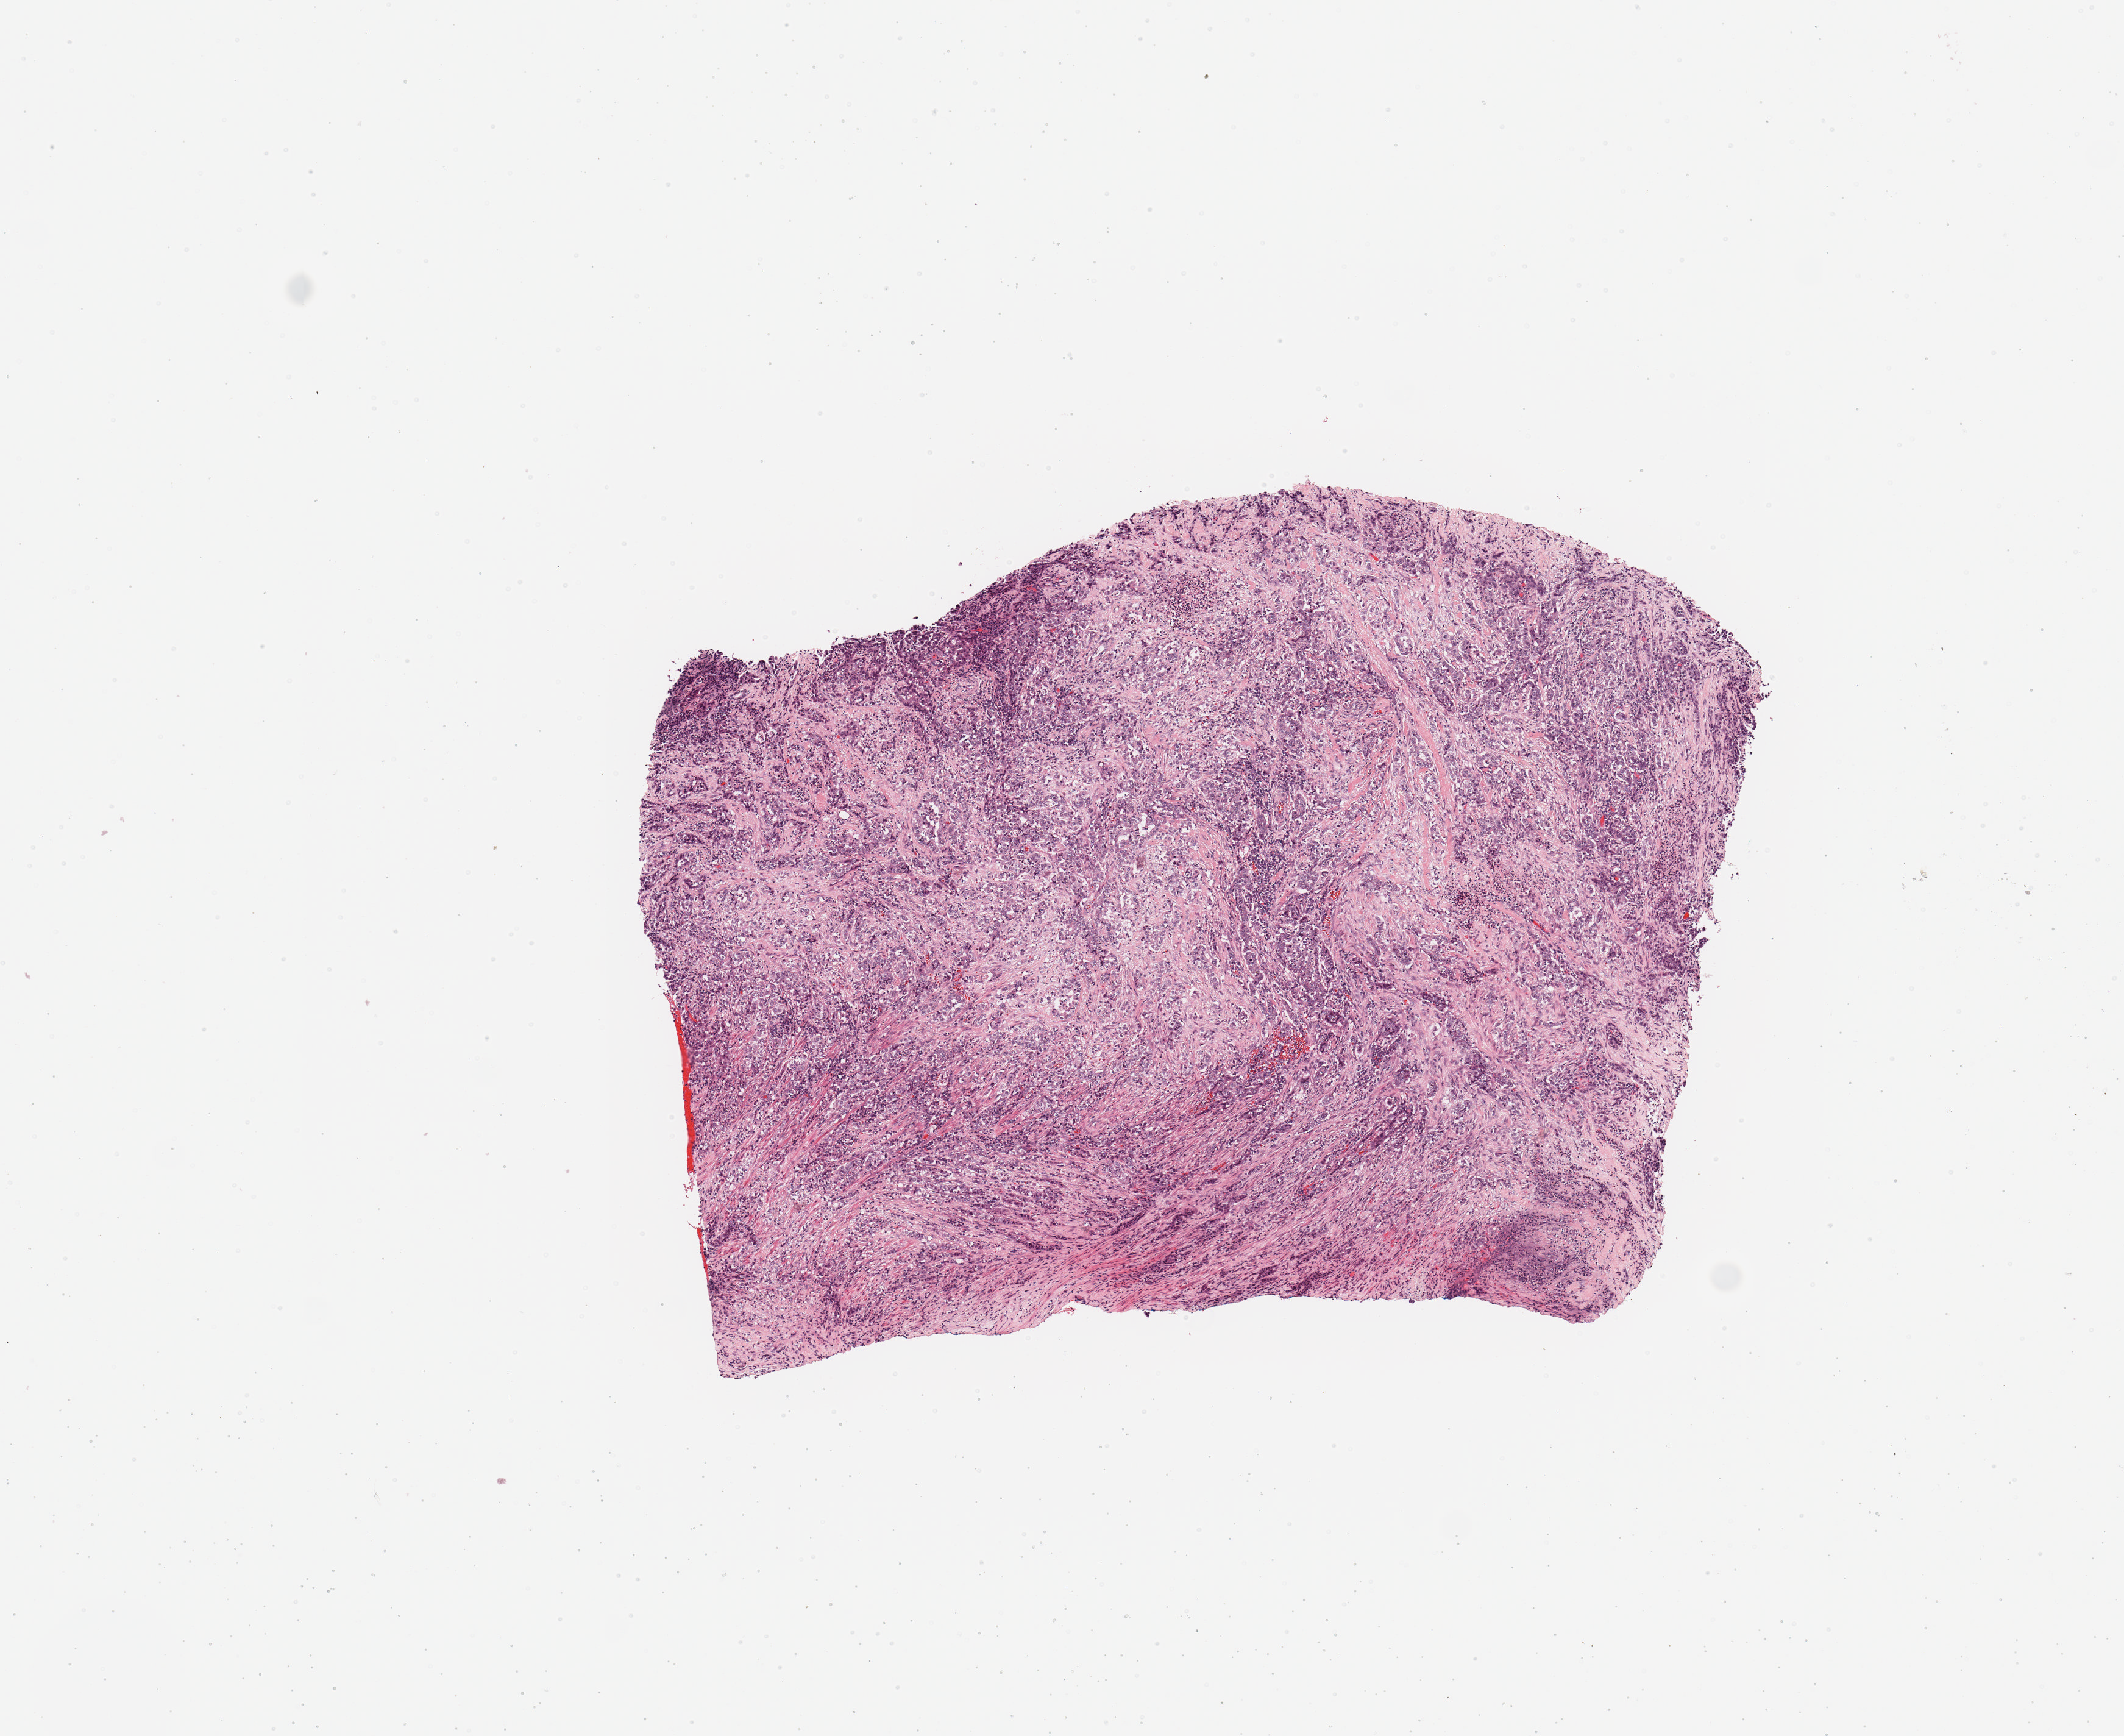
Digitized Hematoxylin and eosin (H&E) stained tissue section (whole slide) — whole scanned area (about 6.9 x 5.6 mm, acquisition: 20x scan) shown as a low-resolution overview; tumour tissue sample, sampled site: lung. Female, 52 y/o. Histologic grade: G2 (moderately differentiated). Pathologist review of this section (percent, as recorded): tumour nuclei 75%, necrosis 5%.
Diagnosis: Adenocarcinoma, NOS. AJCC pathologic stage: IIIA.